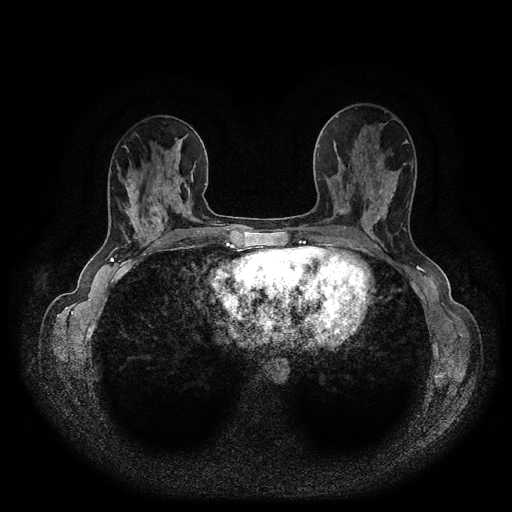
Breast MRI (dynamic contrast-enhanced, multi-phase), one axial slice; slice 40 of 116 in the series (ordered by position); dynamic contrast-enhanced series, time point 2 of 5 at this slice position (early post-contrast); 1.5 T; TE 2.6 ms, TR 5.4 ms; 2 mm slice thickness; 512 × 512 image matrix, field of view 340 × 340 mm. Female patient, age 40 years.
Outlined on this slice (semi-automatic segmentation, software-assisted and operator-edited):
- breast lesion (labelled 'tumour' in the annotation; benign lesions carry a separate 'benign' label): bounding box [x1, y1, x2, y2] px = [336, 207, 349, 216]